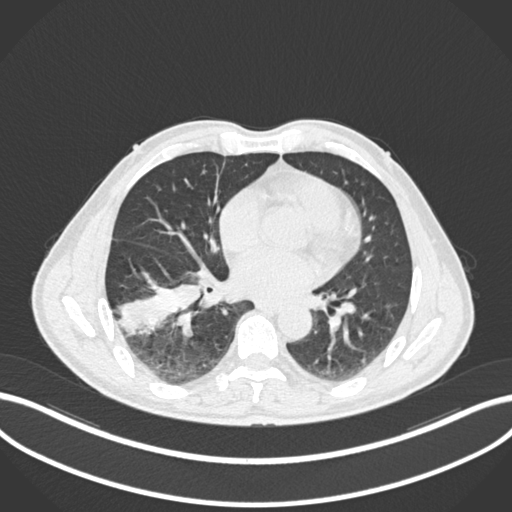
Chest CT, one axial slice; slice 84 of 208 in the series (ordered by position); lung window (W 1500 / L -600 HU); 1 mm slice thickness; 512 × 512 image matrix, field of view 400 × 400 mm. Patient: male, 58 years. From the clinical record (not read from this slice): clinical TNM (as recorded): T3 N0 M0.
Structures marked on this image (rectangle marked by the reading radiologist):
- lung tumour (recorded histology: squamous cell carcinoma): bounding box [x1, y1, x2, y2] px = [115, 278, 203, 343]